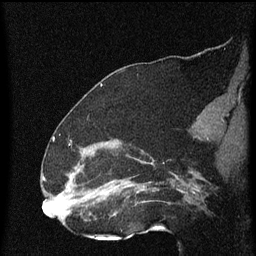
Breast MRI (dynamic contrast-enhanced), one sagittal slice; position 33 of 60 along the scan axis; dynamic contrast-enhanced series, image 2 of 4 at this slice position (ordered by acquisition); 1.5 T; TE 4.2 ms, TR 8 ms; 256 × 256 image matrix. Patient: female, 52 years.
Structures marked on this image (semi-automatically segmented with operator editing):
- analysis volume of interest (the breast-tissue region the enhancement analysis was run in; not a lesion): bounding box <73,148,172,219> (left, top, right, bottom; pixels)
- tumour enhancement mask (voxels above the 70 % enhancement threshold inside the analysis volume of interest): <115,162,153,215>